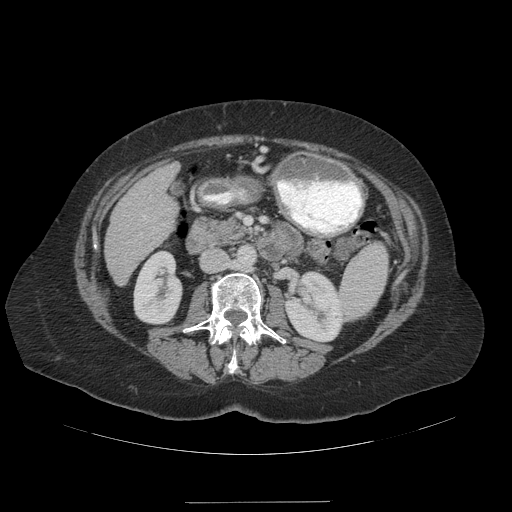
Contrast-enhanced abdominal CT (liver protocol), one axial slice. Position 44 of 99 along the scan axis. 140 kVp. Soft-tissue window (W 400 / L 40 HU). 2.5 mm slice thickness. 512 × 512 image matrix. Case-level facts recorded for this patient, not image findings: diagnosis: hepatocellular carcinoma (patient treated with transarterial chemoembolisation; whether this scan precedes or follows treatment is not stated here); TNM stage (as recorded): Stage-IVA; Child-Pugh class: A; tumour nodularity: multinodular.
Structures marked on this image (semi-automatically segmented with operator editing):
- liver parenchyma outside the tumour (the mass and vessels are separate outlines, so this box may not span the whole liver): bounding box <104,164,178,286> (left, top, right, bottom; pixels)
- liver vessels: <143,215,146,218>